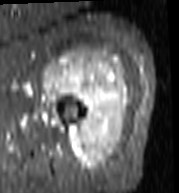
MRI of an extremity soft-tissue mass, one axial slice. Position 78 of 103 along the scan axis. STIR. MR volume resampled by the dataset authors to the PET/CT grid (not the native acquisition matrix). 3.27 mm slice thickness. 179 × 193 image matrix. Female patient. Case-level facts recorded for this patient, not image findings: histological type: undifferentiated – high grade; grade: high; site of the primary tumour: left thigh.
Annotated regions visible in this slice (expert contour drawn on MRI and transferred to this co-registered scan by the dataset authors):
- gross tumour volume including surrounding oedema: bounding box [x1, y1, x2, y2] px = [41, 51, 129, 170]
- gross tumour volume (mass): [43, 51, 128, 170]